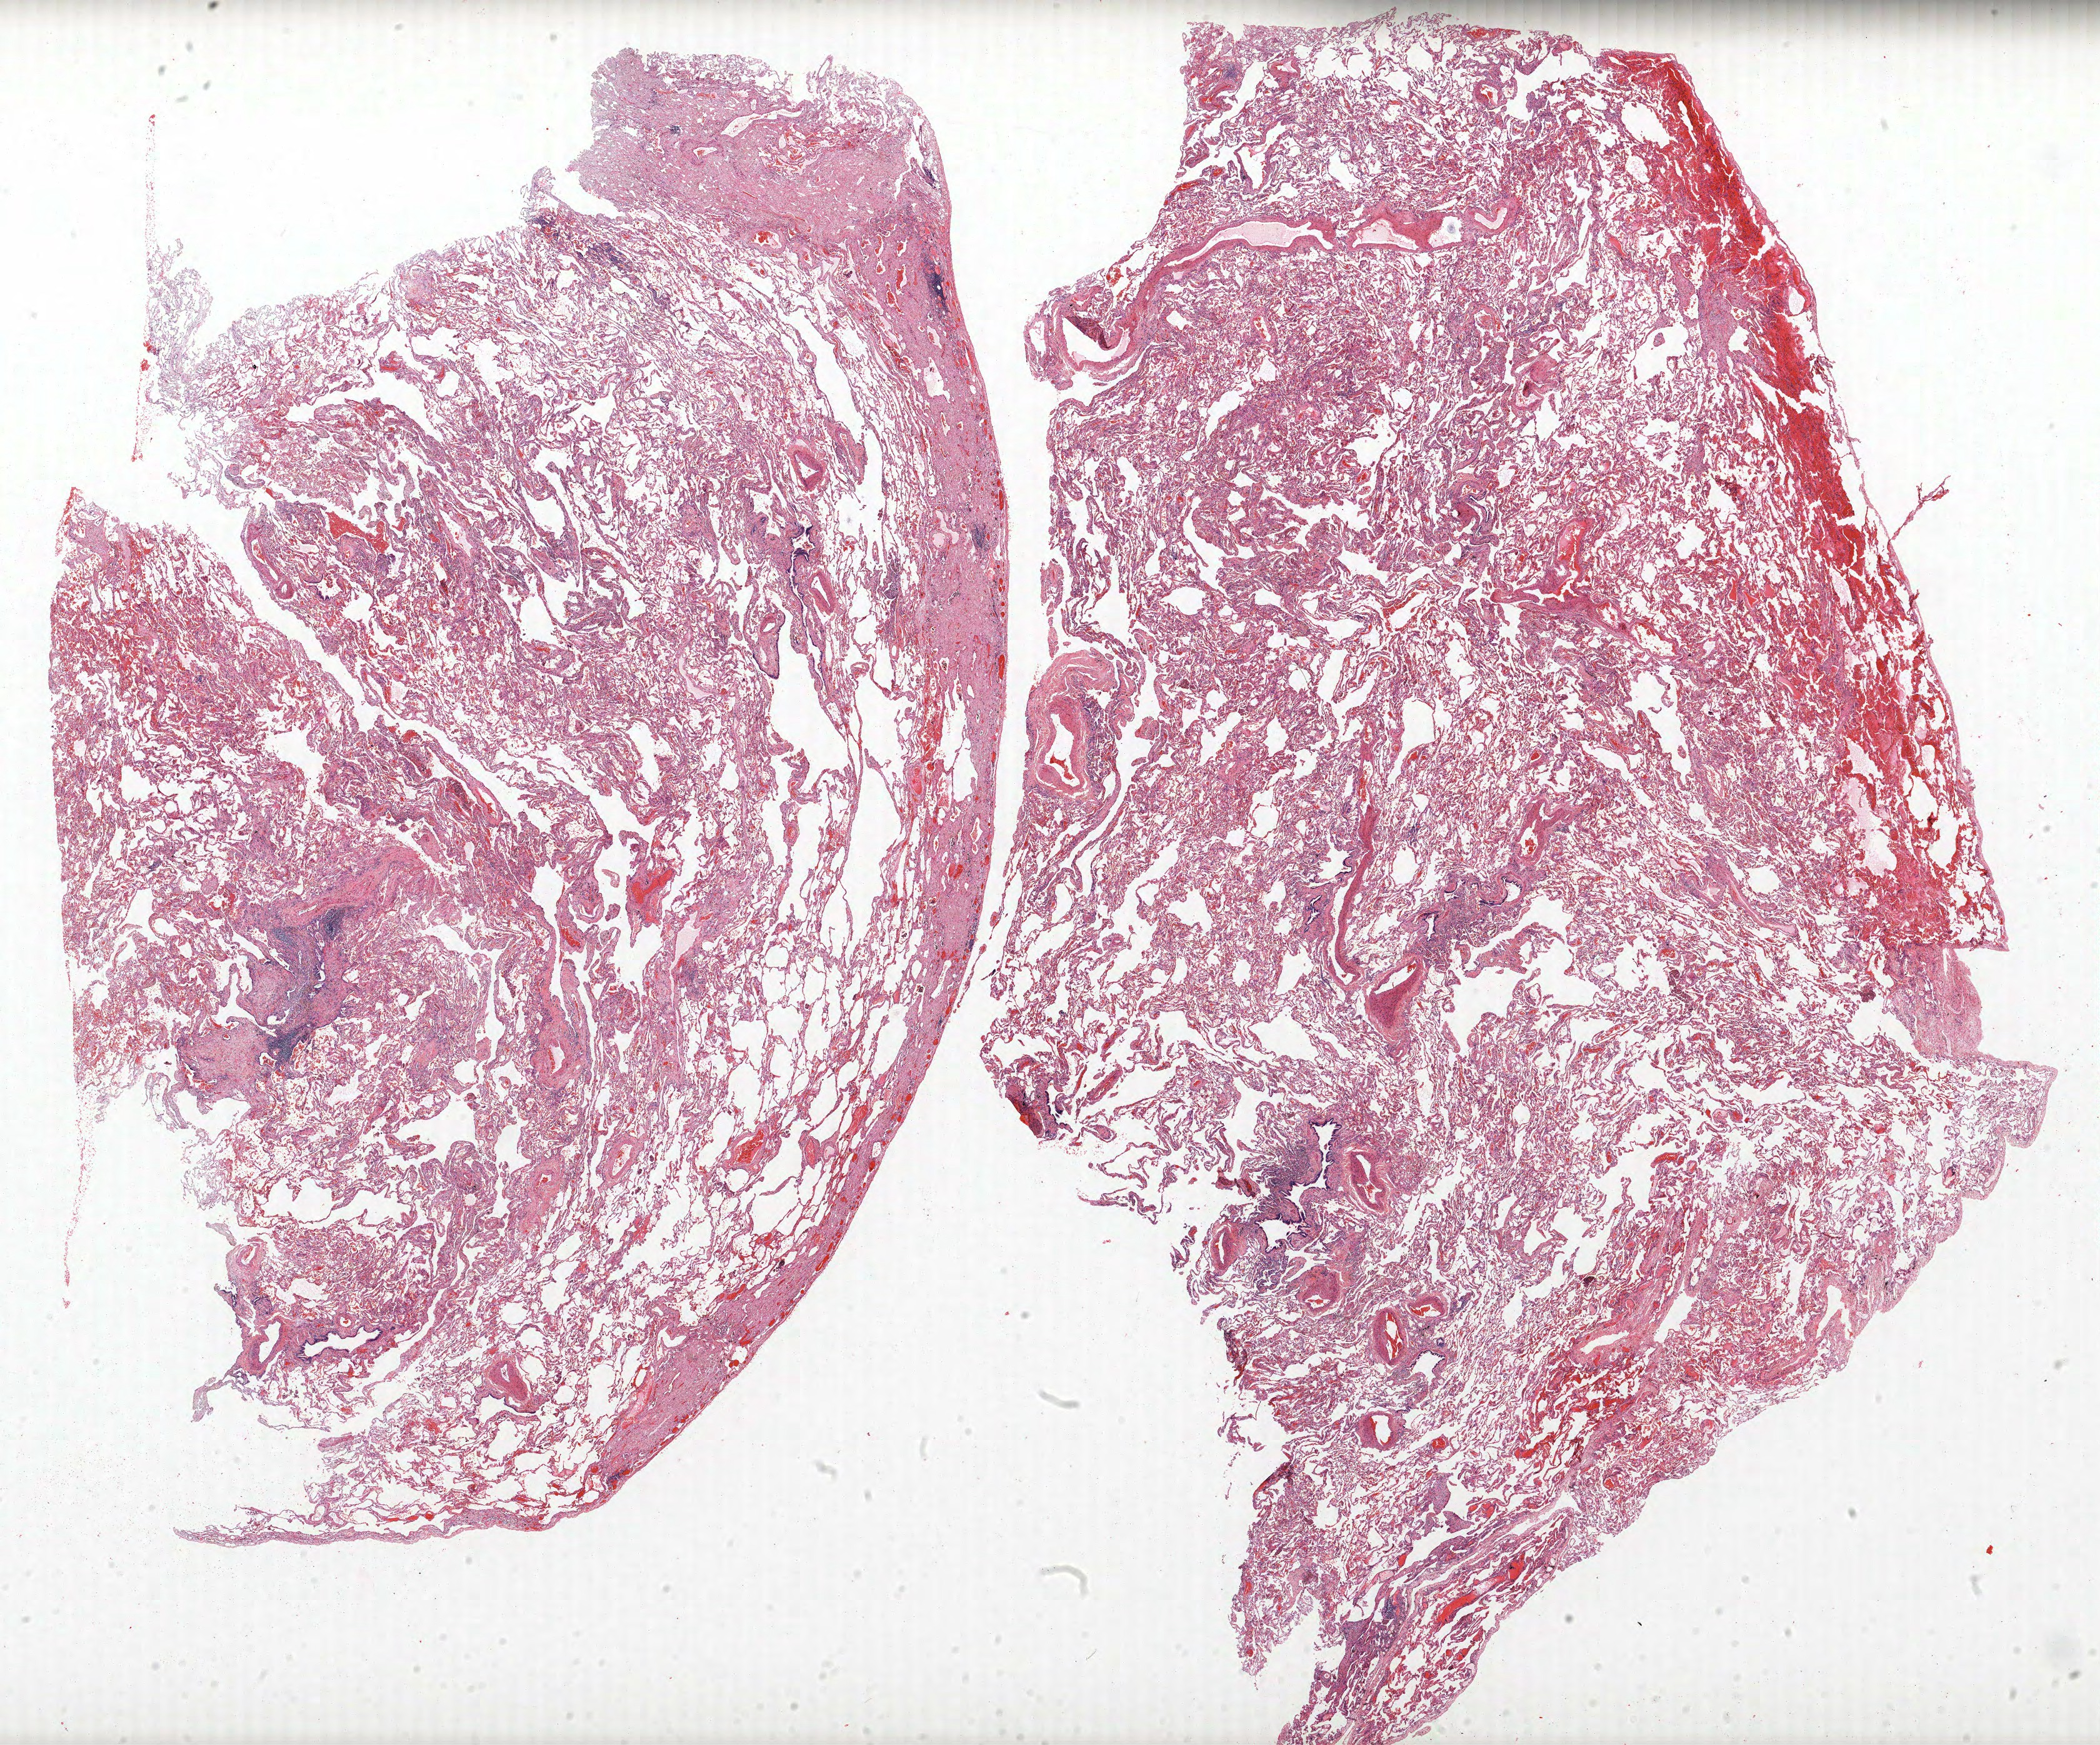
Whole-slide histology image, H&E — shown as a low-resolution overview of the whole scanned area (about 26.9 x 22.3 mm, from a 40x scan). FFPE section. Lung. Male, age 63 at enrolment. Current smoker at enrolment. Grade: moderately differentiated (G2).
Tumour size (pathology): 17 mm. Primary tumour location (clinical record): right upper lobe. Stage (AJCC 6th edition): IIIB. Participant's lung-cancer diagnosis: Adenocarcinoma, NOS (ICD-O-3 8140/3).